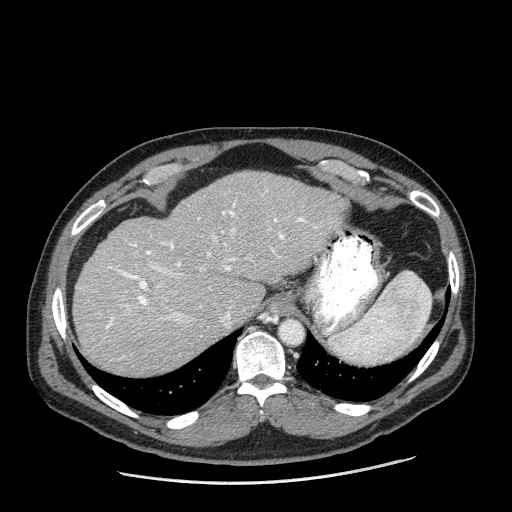
Contrast-enhanced abdominal CT (liver protocol), one axial slice; position 143 of 198 along the scan axis; reconstruction kernel STANDARD; 120 kVp; one of 2 acquisitions stored at this slice position; soft-tissue window (W 400 / L 40 HU); 2.5 mm slice thickness; 512 × 512 image matrix, field of view 400 × 400 mm. From the clinical record (not read from this slice): diagnosis: hepatocellular carcinoma (patient treated with transarterial chemoembolisation; whether this scan precedes or follows treatment is not stated here); TNM stage (as recorded): Stage-II; Child-Pugh class: A; tumour differentiation: moderately differentiated; tumour nodularity: multinodular.
Annotated regions visible in this slice (semi-automatically segmented with operator editing):
- liver parenchyma outside the tumour (the mass and vessels are separate outlines, so this box may not span the whole liver): bounding box [x1, y1, x2, y2] px = [72, 170, 346, 376]
- liver vessels: [106, 201, 316, 357]